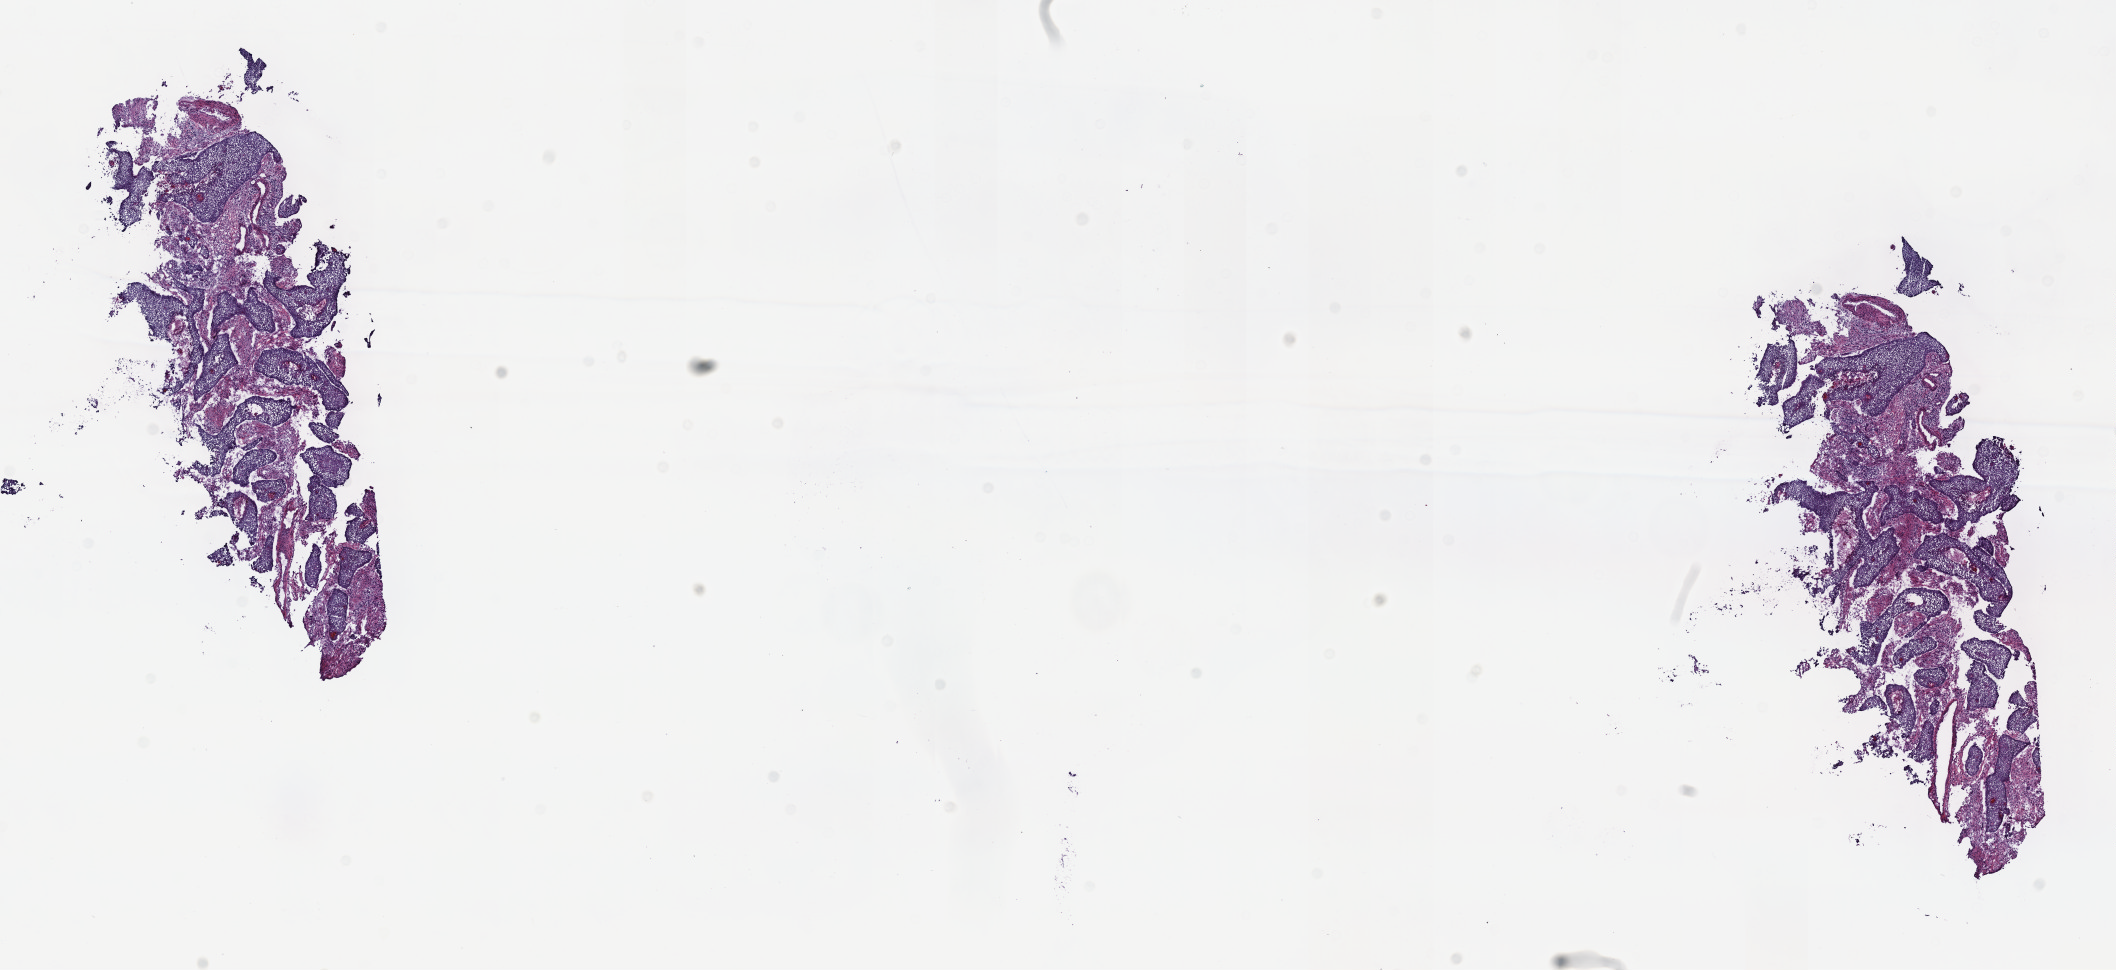
Whole-slide histology image, H&E, low-resolution overview of the scanned area, about 17.1 x 7.8 mm (from a 40x scan). Frozen section. Cervix, primary tumour sample. Female, age 41 years at initial diagnosis. Histologic grade: G2 (moderately differentiated). Slide review estimates, as recorded: tumour cells 70%, tumour nuclei 70%, normal cells 0%, stromal cells 20%, necrosis 10%. Infiltration values recorded for this section: lymphocyte infiltration 60%, monocyte infiltration 20%, neutrophil infiltration 40%.
FIGO stage: IIB. Diagnosis: Squamous cell carcinoma, keratinizing, NOS (cervix uteri).